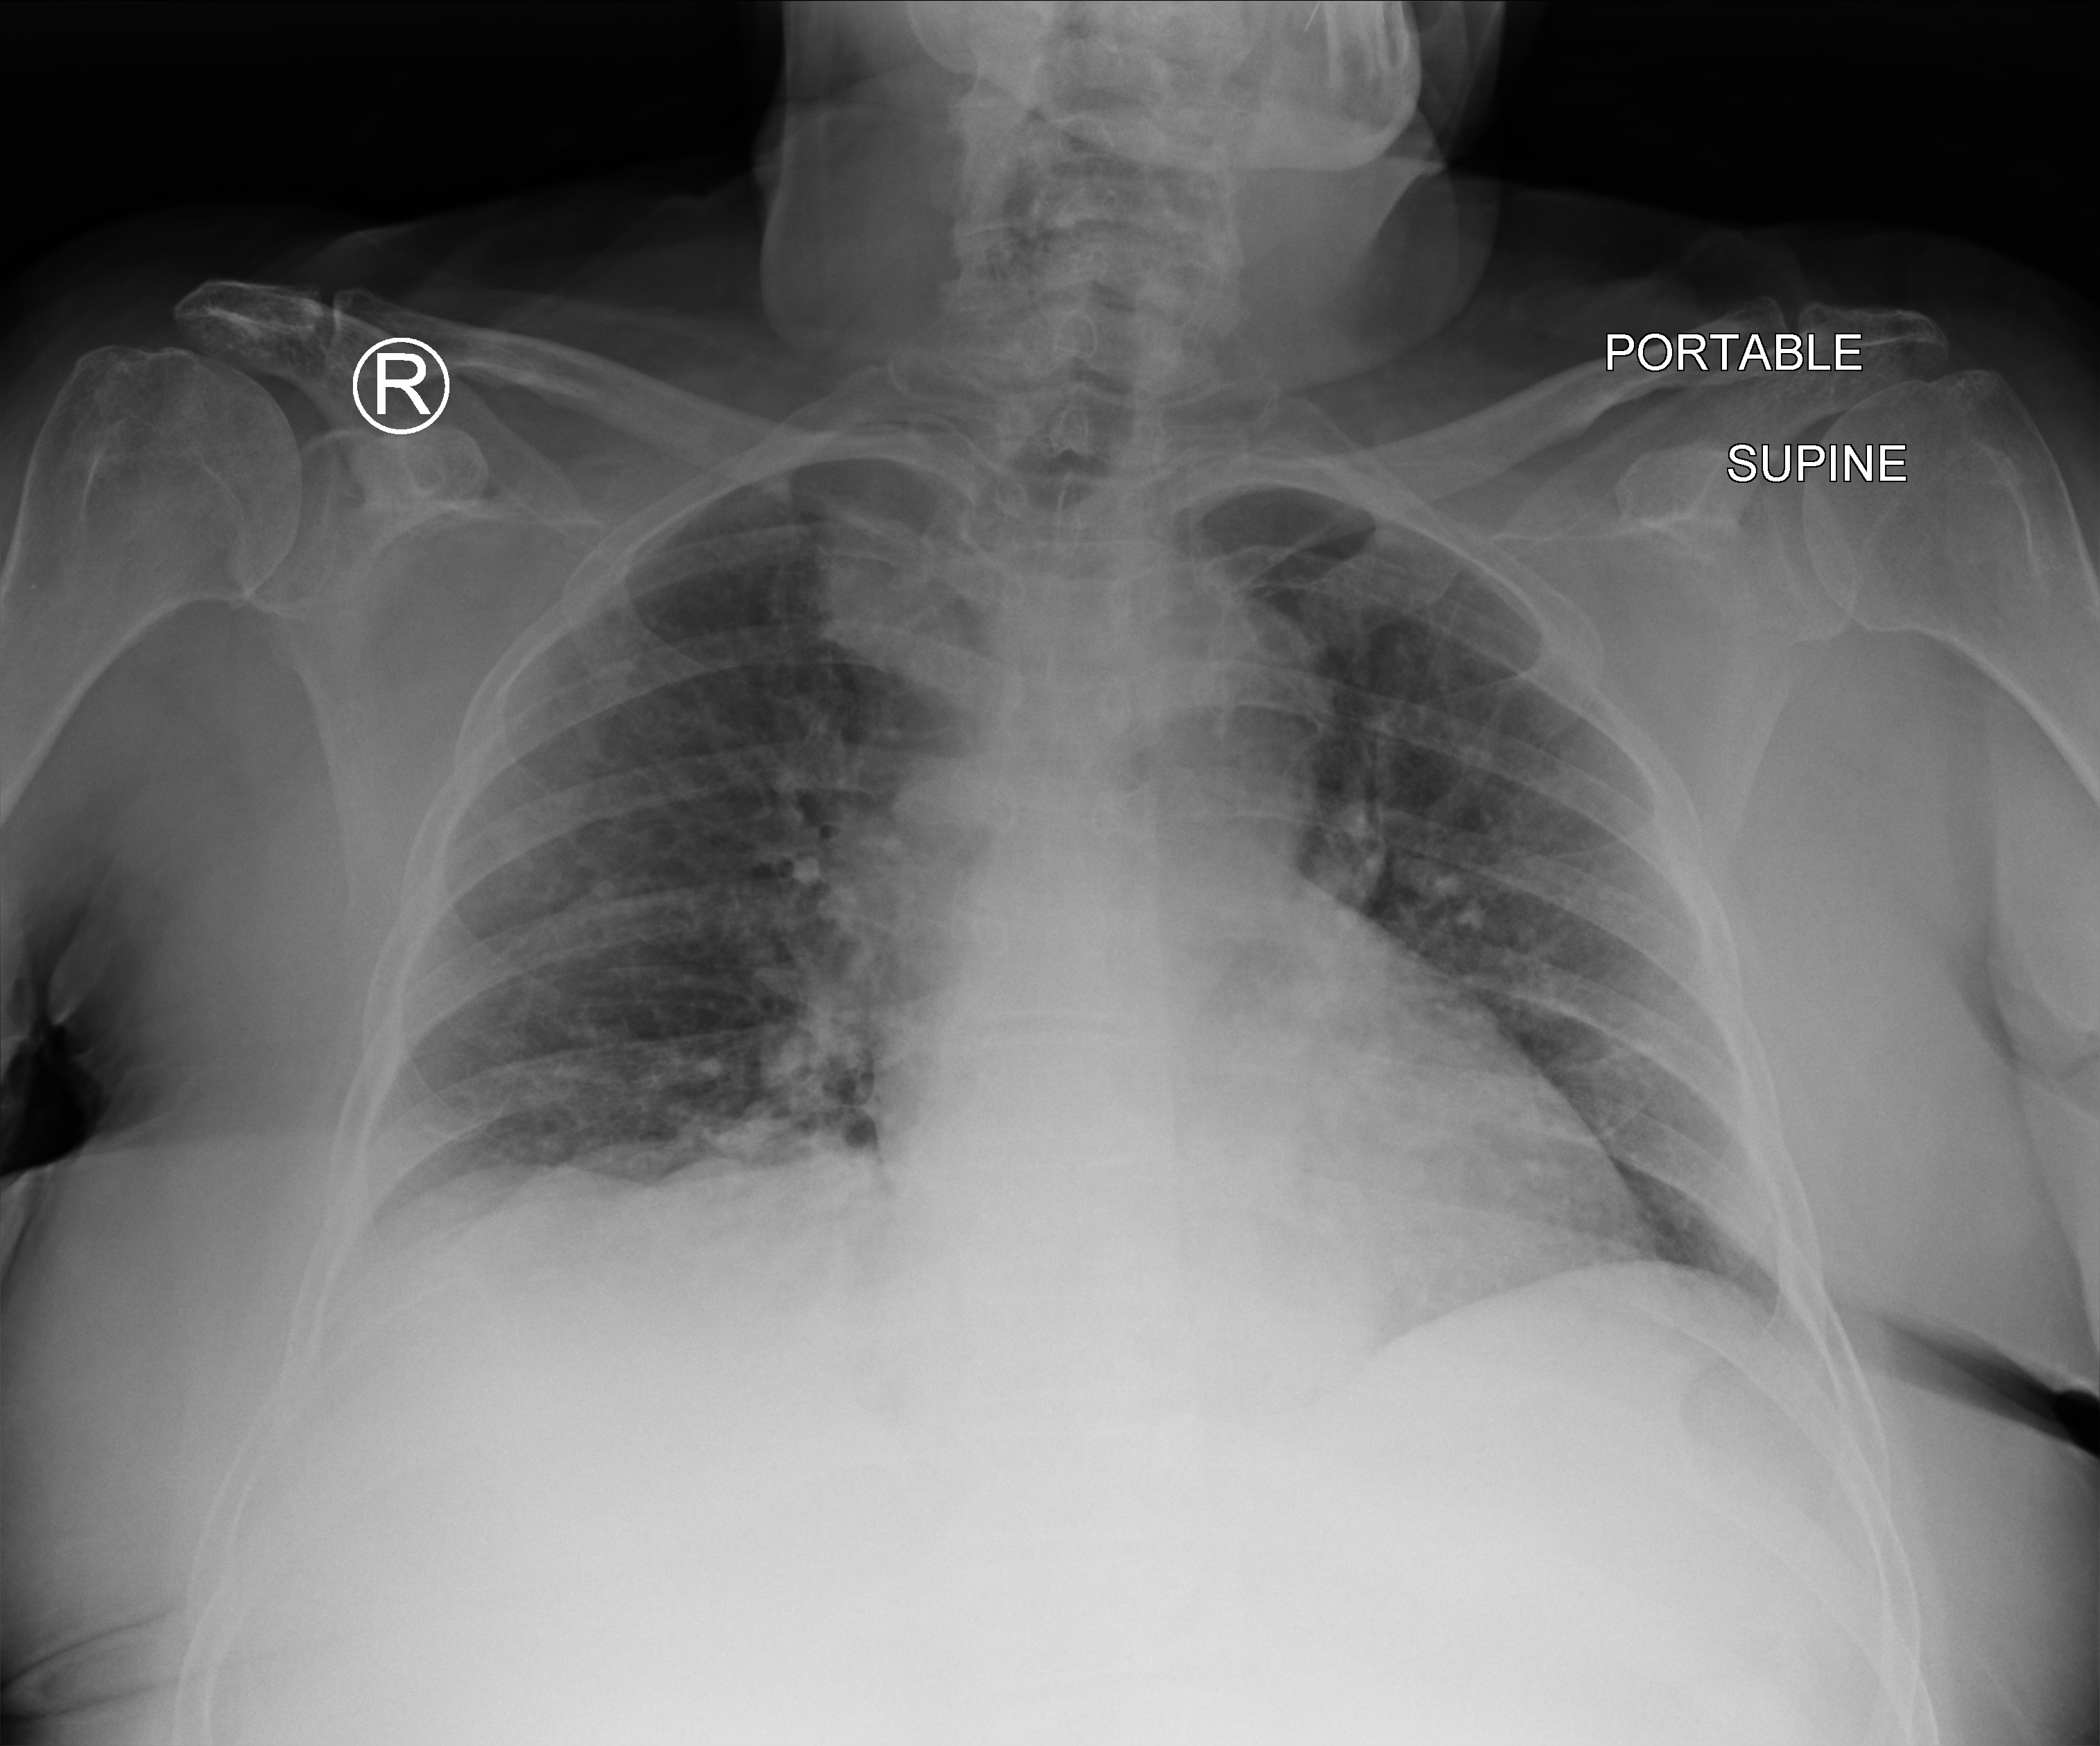
Portable chest radiograph; anteroposterior (AP) projection. Female patient hospitalised with COVID-19, age 75–90 years.
Admission-level facts for this patient (not findings on this image; timing relative to this image not recorded): diabetes (admission record): no; admitted to intensive care during this hospital stay: no; mechanically ventilated during this hospital stay: no.